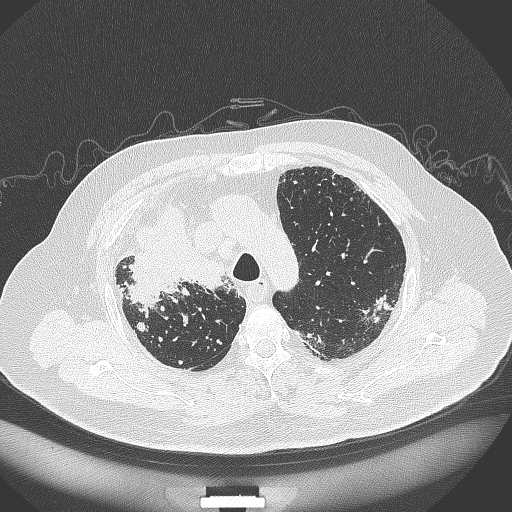
Chest CT, one axial slice. Slice 274 of 384 in the series (ordered by position). 120 kVp. Lung window (W 1500 / L -600 HU). 1 mm slice thickness. 512 × 512 image matrix, field of view 400 × 400 mm. Patient: male, 69 years. Case-level facts recorded for this patient, not image findings: clinical TNM (as recorded): T4 N3 M1.
Structures marked on this image (bounding box drawn by a radiologist):
- lung tumour (recorded histology: adenocarcinoma): bounding box (x1, y1, x2, y2) in pixels: (123, 207, 226, 307)